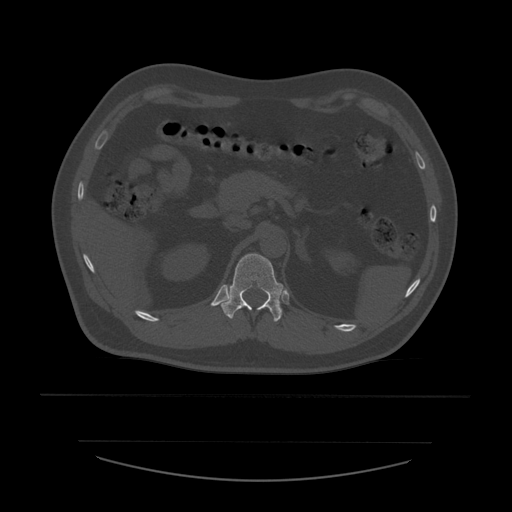
CT including the spine, one axial slice. Position 254 of 532 along the scan axis. Bone window (W 1800 / L 400 HU). 512 × 512 image matrix, field of view 441 × 441 mm. Patient age 44 years. Case-level facts recorded for this patient, not image findings: primary cancer: soft tissue sarcoma.
Structures marked on this image (semi-automatically segmented with operator editing):
- T12 vertebra: box from (x=221, y=254) to (x=284, y=322) px